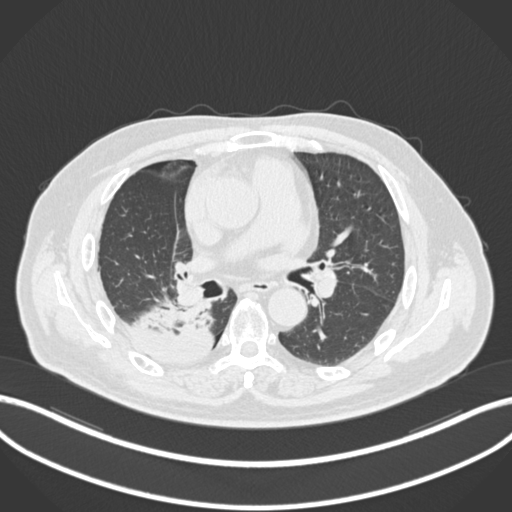
Chest CT, one axial slice; slice 100 of 218 in the series (ordered by position); reconstruction kernel B30f; 120 kVp; lung window (W 1500 / L -600 HU); 1 mm slice thickness; 512 × 512 image matrix. Patient: male, 68 years. Case-level facts recorded for this patient, not image findings: clinical TNM (as recorded): T2a N0 M0.
Structures marked on this image (rectangle marked by the reading radiologist):
- lung tumour (recorded histology: adenocarcinoma): bounding box [x1, y1, x2, y2] px = [132, 296, 221, 366]